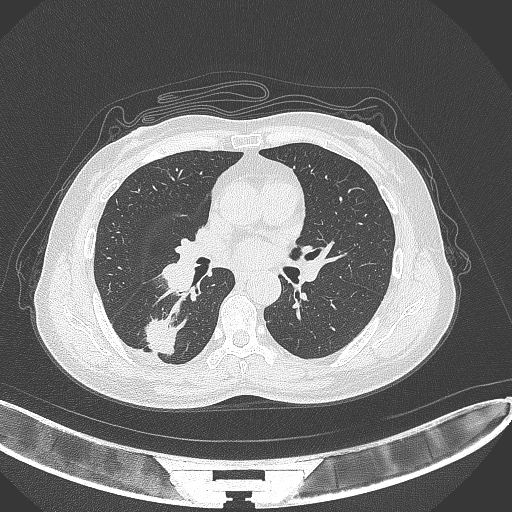
Chest CT, one axial slice. Slice 161 of 352 in the series (ordered by position). Reconstruction kernel B70f. 120 kVp. Lung window (W 1500 / L -600 HU). 1 mm slice thickness. 512 × 512 image matrix, field of view 400 × 400 mm. Female patient, age 55 years. Case-level facts recorded for this patient, not image findings: clinical TNM (as recorded): T1c N1 M0.
Annotated regions visible in this slice (bounding box drawn by a radiologist):
- lung tumour (recorded histology: adenocarcinoma): box from (x=141, y=317) to (x=180, y=358) px